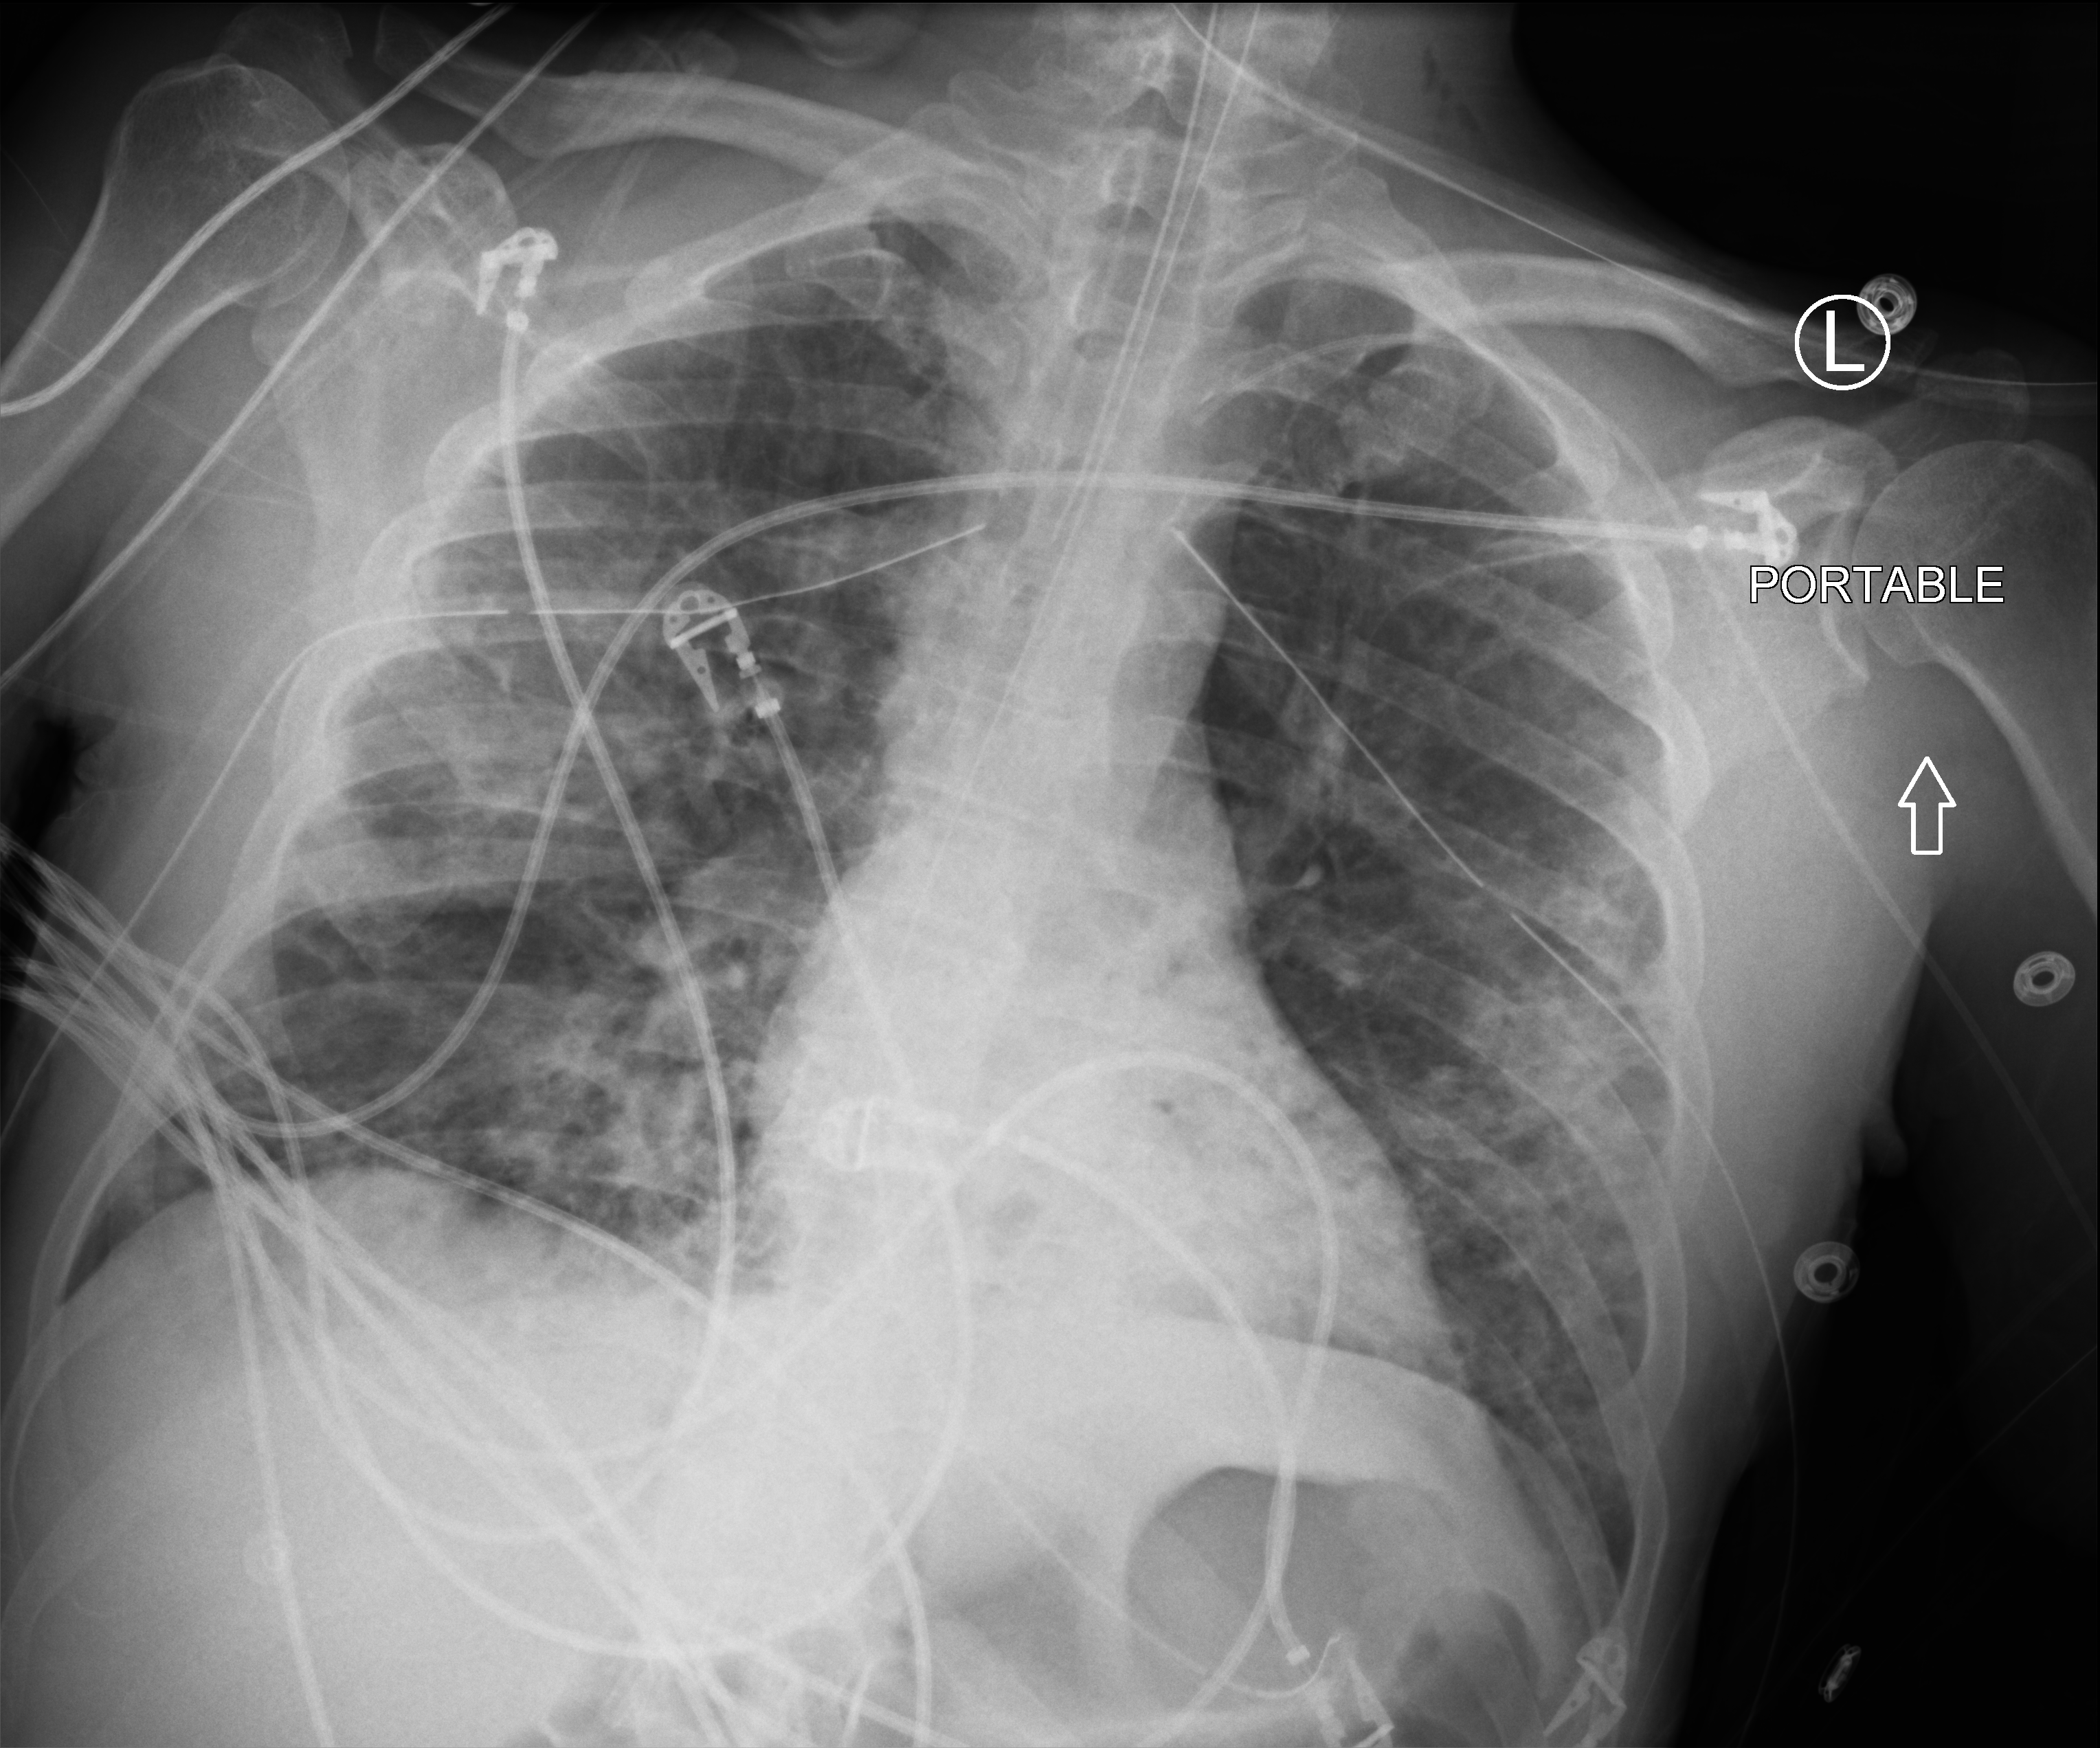
Bedside chest radiograph (computed radiography); anteroposterior (AP) projection. Male patient hospitalised with COVID-19, age 18–59 years.
Admission-level facts for this patient (not findings on this image; timing relative to this image not recorded):
- mechanically ventilated during this hospital stay: yes
- admitted to intensive care during this hospital stay: yes
- smoking status (admission record): never